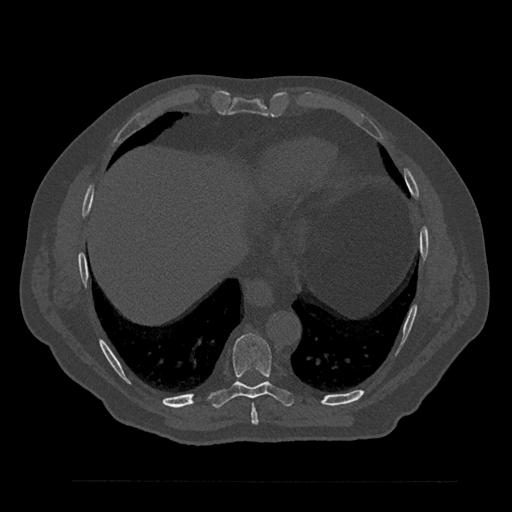
CT including the spine, one axial slice. Slice 408 of 797 in the series (ordered by position). Reconstruction kernel Br40s/3. Bone window (W 1800 / L 400 HU). 512 × 512 image matrix, field of view 430 × 430 mm. Male patient, age 61 years. From the clinical record (not read from this slice): primary cancer: prostate.
Outlined on this slice (semi-automatically segmented with operator editing):
- T8 vertebra: bounding box (x1, y1, x2, y2) in pixels: (251, 404, 259, 425)
- T9 vertebra: (209, 334, 294, 408)